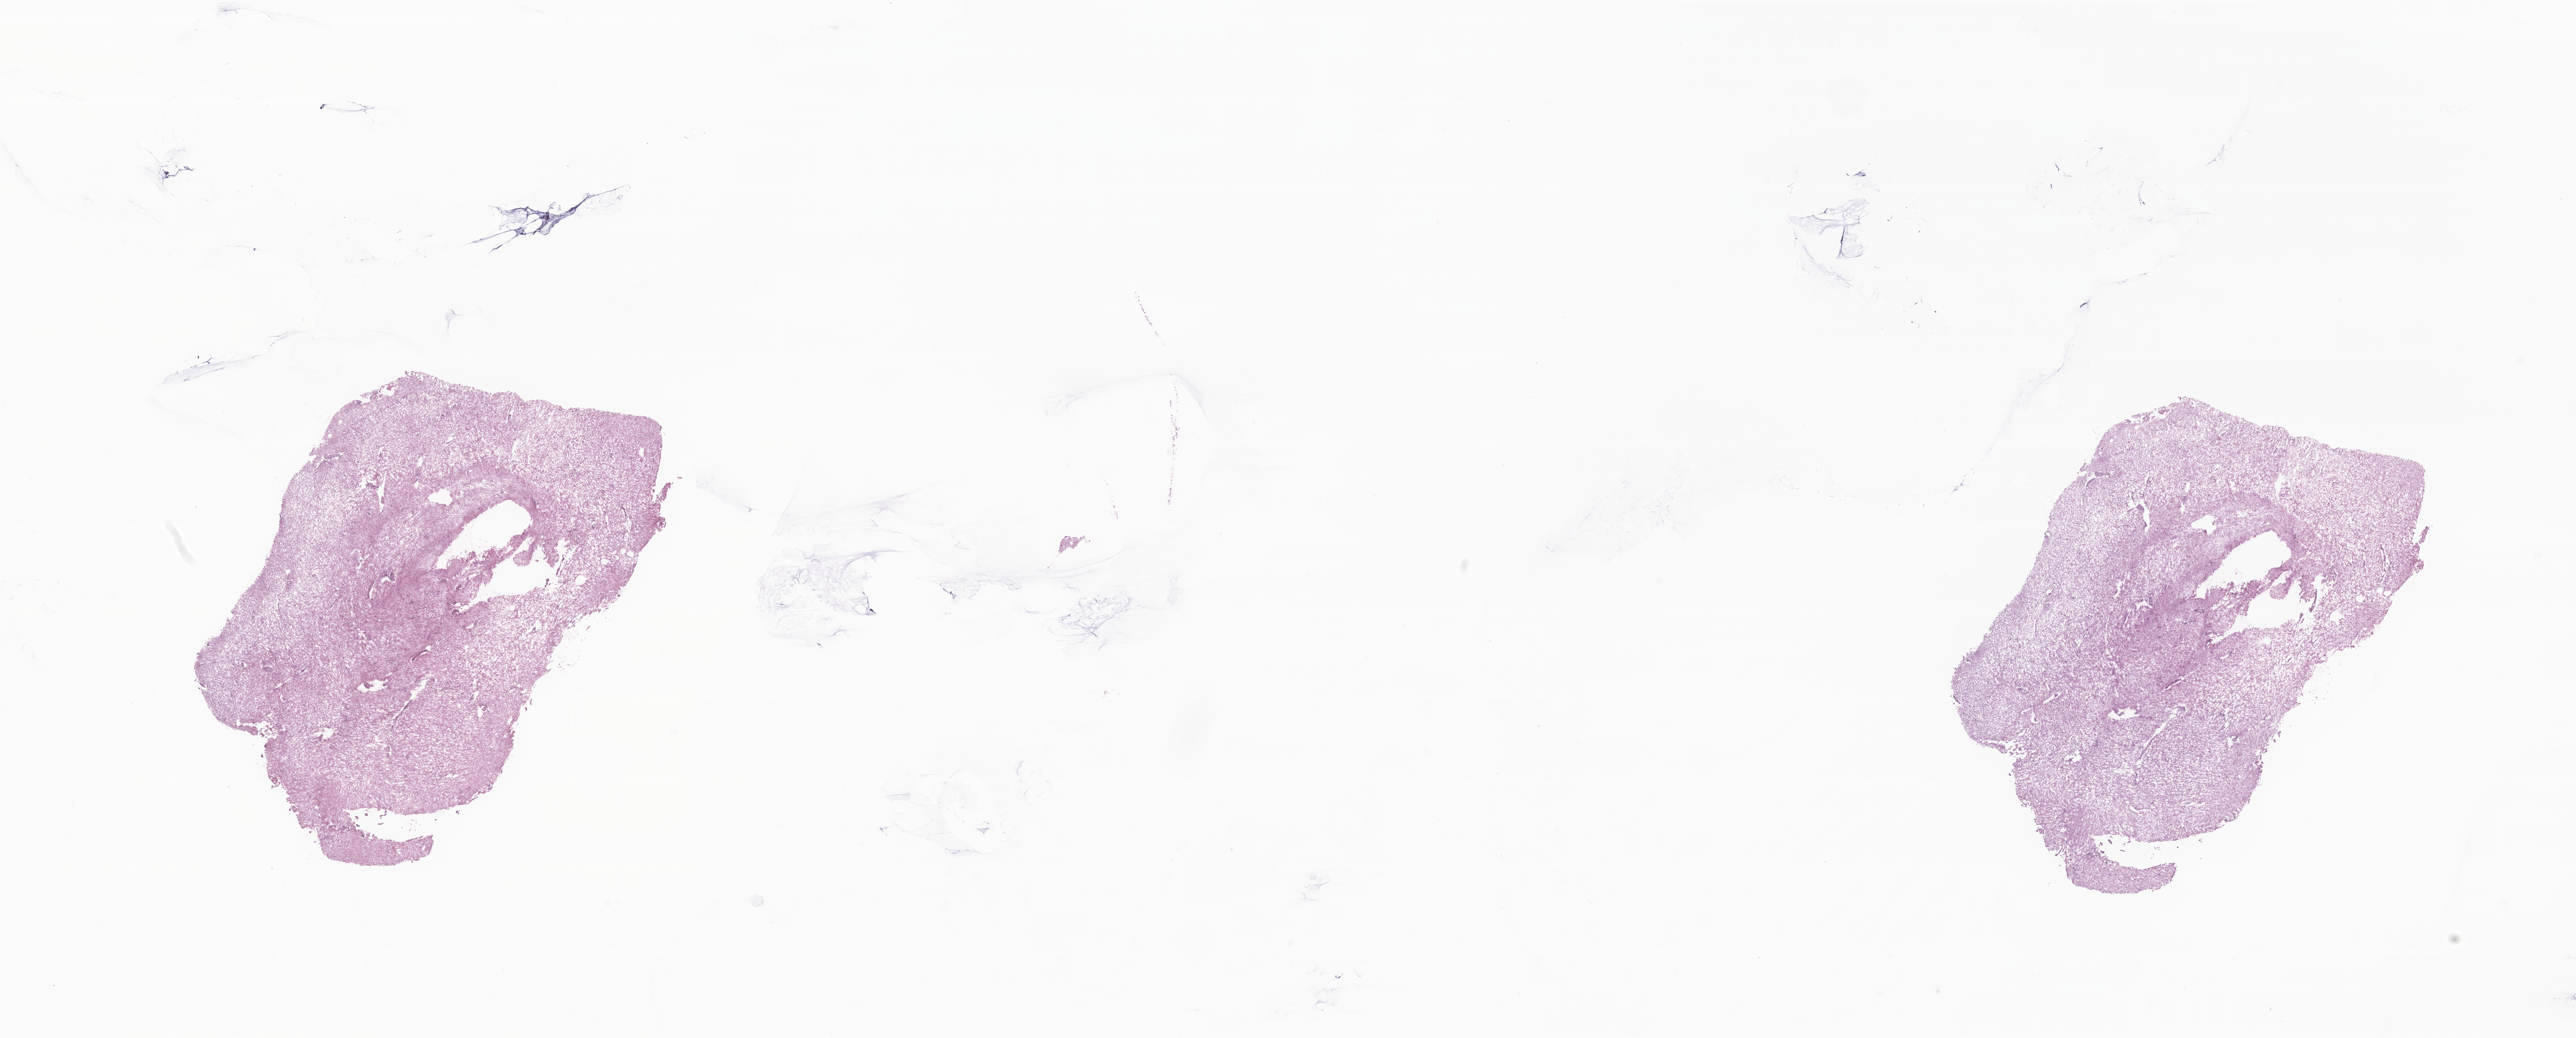
Whole-slide image, H&E stain of tumor tissue from the brain stem — whole scanned area (about 32.4 x 13.1 mm) shown as a low-resolution overview, frozen section. Patient: male, age 204 months (17 years).
Diagnosis: Glioma, malignant.